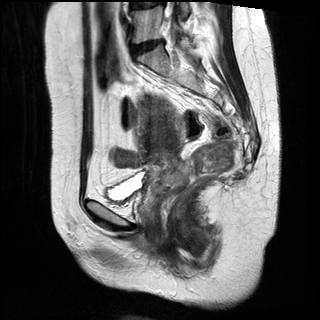
Pelvic MRI for cervical cancer, one sagittal slice; slice 15 of 34 in the series (ordered by position); T2-weighted; 1.5 T; TE 89 ms, TR 3320 ms; 4 mm slice thickness; 320 × 320 image matrix, field of view 260 × 260 mm. Patient: female, 49 years.
Structures marked on this image (manually delineated by an expert):
- uterus and cervix: box from (x=136, y=92) to (x=191, y=197) px